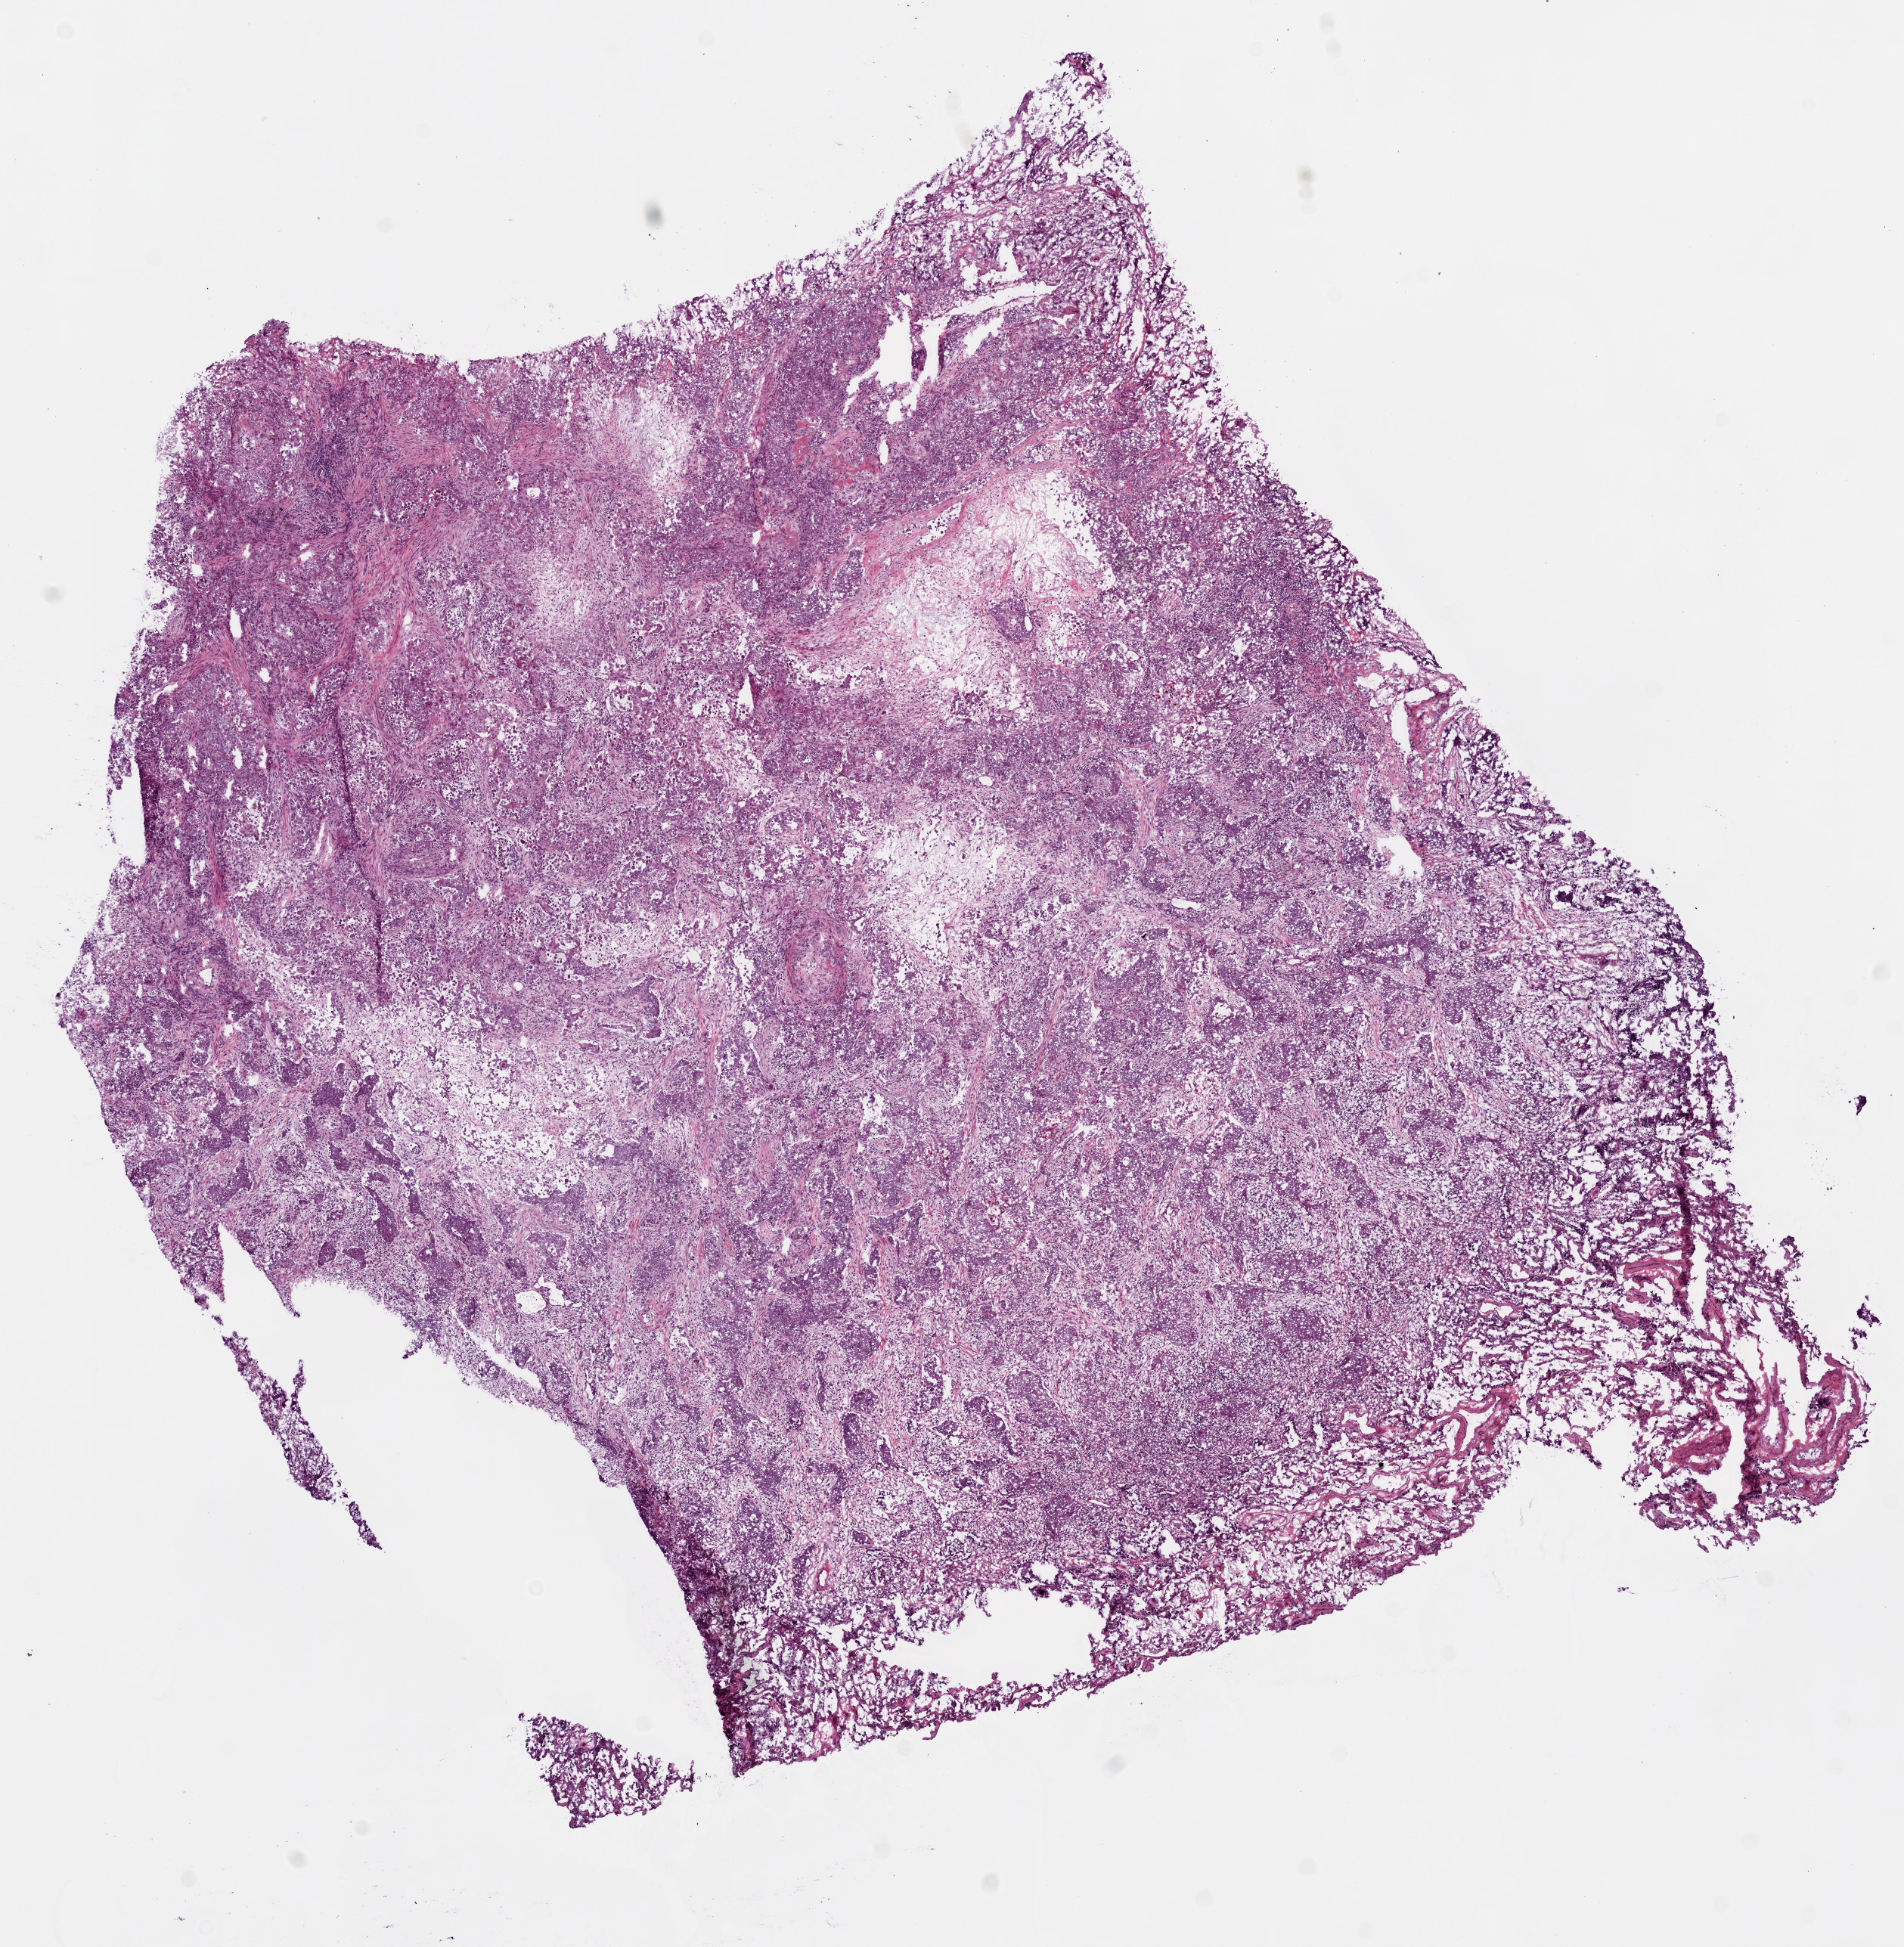
Digitized Hematoxylin and eosin (H&E) stained tissue section (whole slide), a low-resolution overview of the entire scanned area, about 10.2 x 10.4 mm (from a 20x scan). Frozen section. Sample: primary tumour, lung. Male, age 74 years at initial diagnosis. Pathologist review of this section (percent, as recorded): tumour cells 75%, tumour nuclei 75%, normal cells 5%, stromal cells 10%, necrosis 10%.
AJCC pathologic stage: IIB (6th edition). Laterality: right. Pathologic diagnosis: Adenocarcinoma with mixed subtypes (upper lobe, lung). TNM: T2 N1 M0.